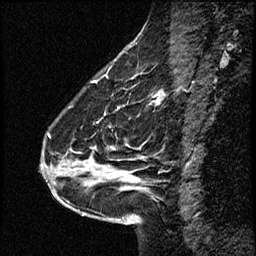
Breast MRI (dynamic contrast-enhanced), one sagittal slice; slice 20 of 50 in the series (ordered by position); dynamic contrast-enhanced study with each time point stored as its own series, time point 2 of 4 at this slice position (early post-contrast, ordered by acquisition time); 1.5 T; TE 4.2 ms, TR 17.5 ms; 256 × 256 image matrix. From the clinical record (not read from this slice): setting: breast cancer imaged before/during neoadjuvant chemotherapy.
Outlined on this slice (semi-automatic segmentation, software-assisted and operator-edited):
- analysis volume of interest (the breast-tissue region the enhancement analysis was run in; not a lesion): bounding box (x1, y1, x2, y2) in pixels: (52, 98, 158, 207)
- tumour enhancement mask (voxels above the 100 % enhancement threshold inside the analysis volume of interest): (87, 101, 158, 180)